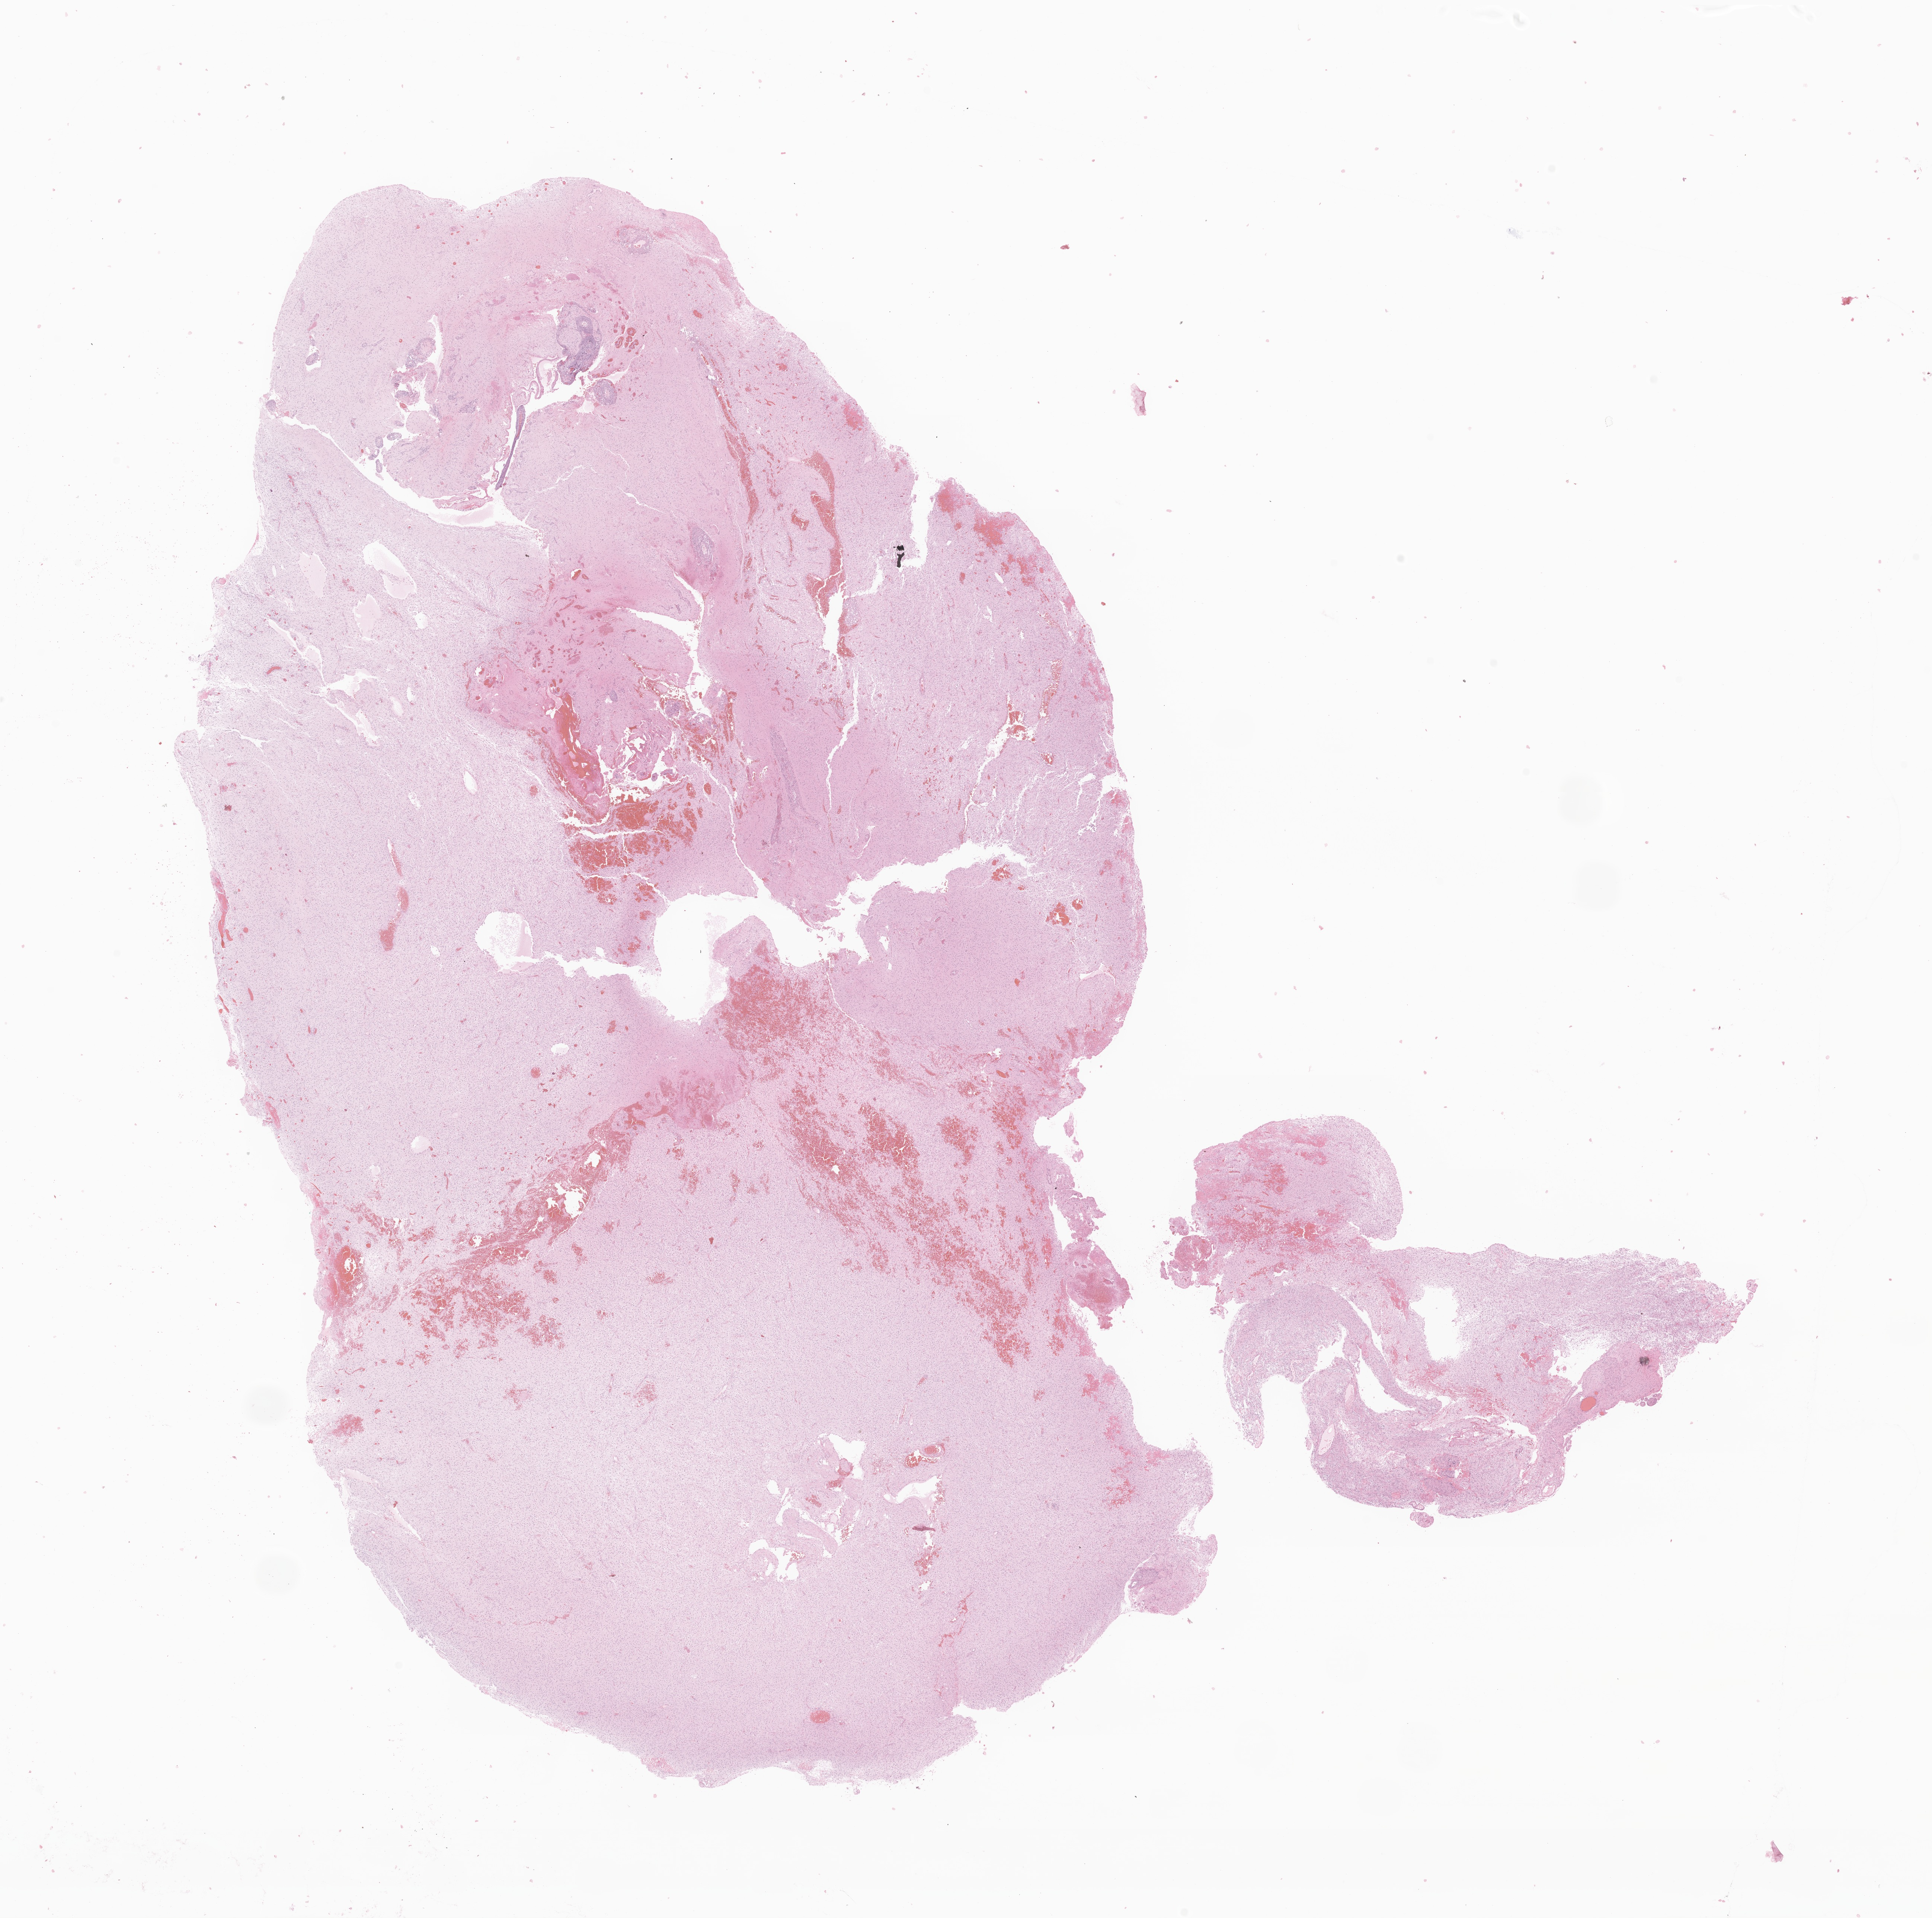
Whole-slide image, hematoxylin and eosin (H&E) stain of tumor tissue from the brain — a low-resolution overview of the entire scanned area, about 21.9 x 21.7 mm; formalin-fixed paraffin-embedded section. Patient: male, age 108 months.
Recorded diagnosis: Neoplasm, malignant.